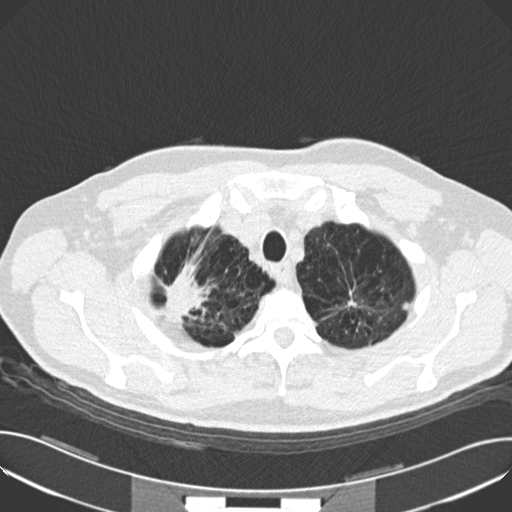
Low-dose screening chest CT, one axial slice. Position 141 of 159 along the scan axis. Reconstruction kernel B30f. 120 kVp. Lung window (W 1500 / L -600 HU). 2 mm slice thickness. 512 × 512 image matrix, field of view 380 × 380 mm.
Structures marked on this image (manually delineated by an expert):
- lesion 1 (tumor, upper lobe of right lung): bounding box <162,274,207,320> (left, top, right, bottom; pixels)